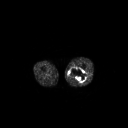
FDG PET of an extremity soft-tissue mass (from a PET/CT study), one axial slice. Position 217 of 267 along the scan axis. 3.27 mm slice thickness. 128 × 128 image matrix. Male patient, age 44 years. Case-level facts recorded for this patient, not image findings: histological type: undifferentiated pleomorphic liposarcoma; grade: high; site of the primary tumour: left thigh.
Structures marked on this image (expert contour drawn on MRI and transferred to this co-registered scan by the dataset authors):
- gross tumour volume including surrounding oedema: bounding box (x1, y1, x2, y2) in pixels: (69, 67, 87, 83)
- gross tumour volume (mass): (69, 67, 87, 83)